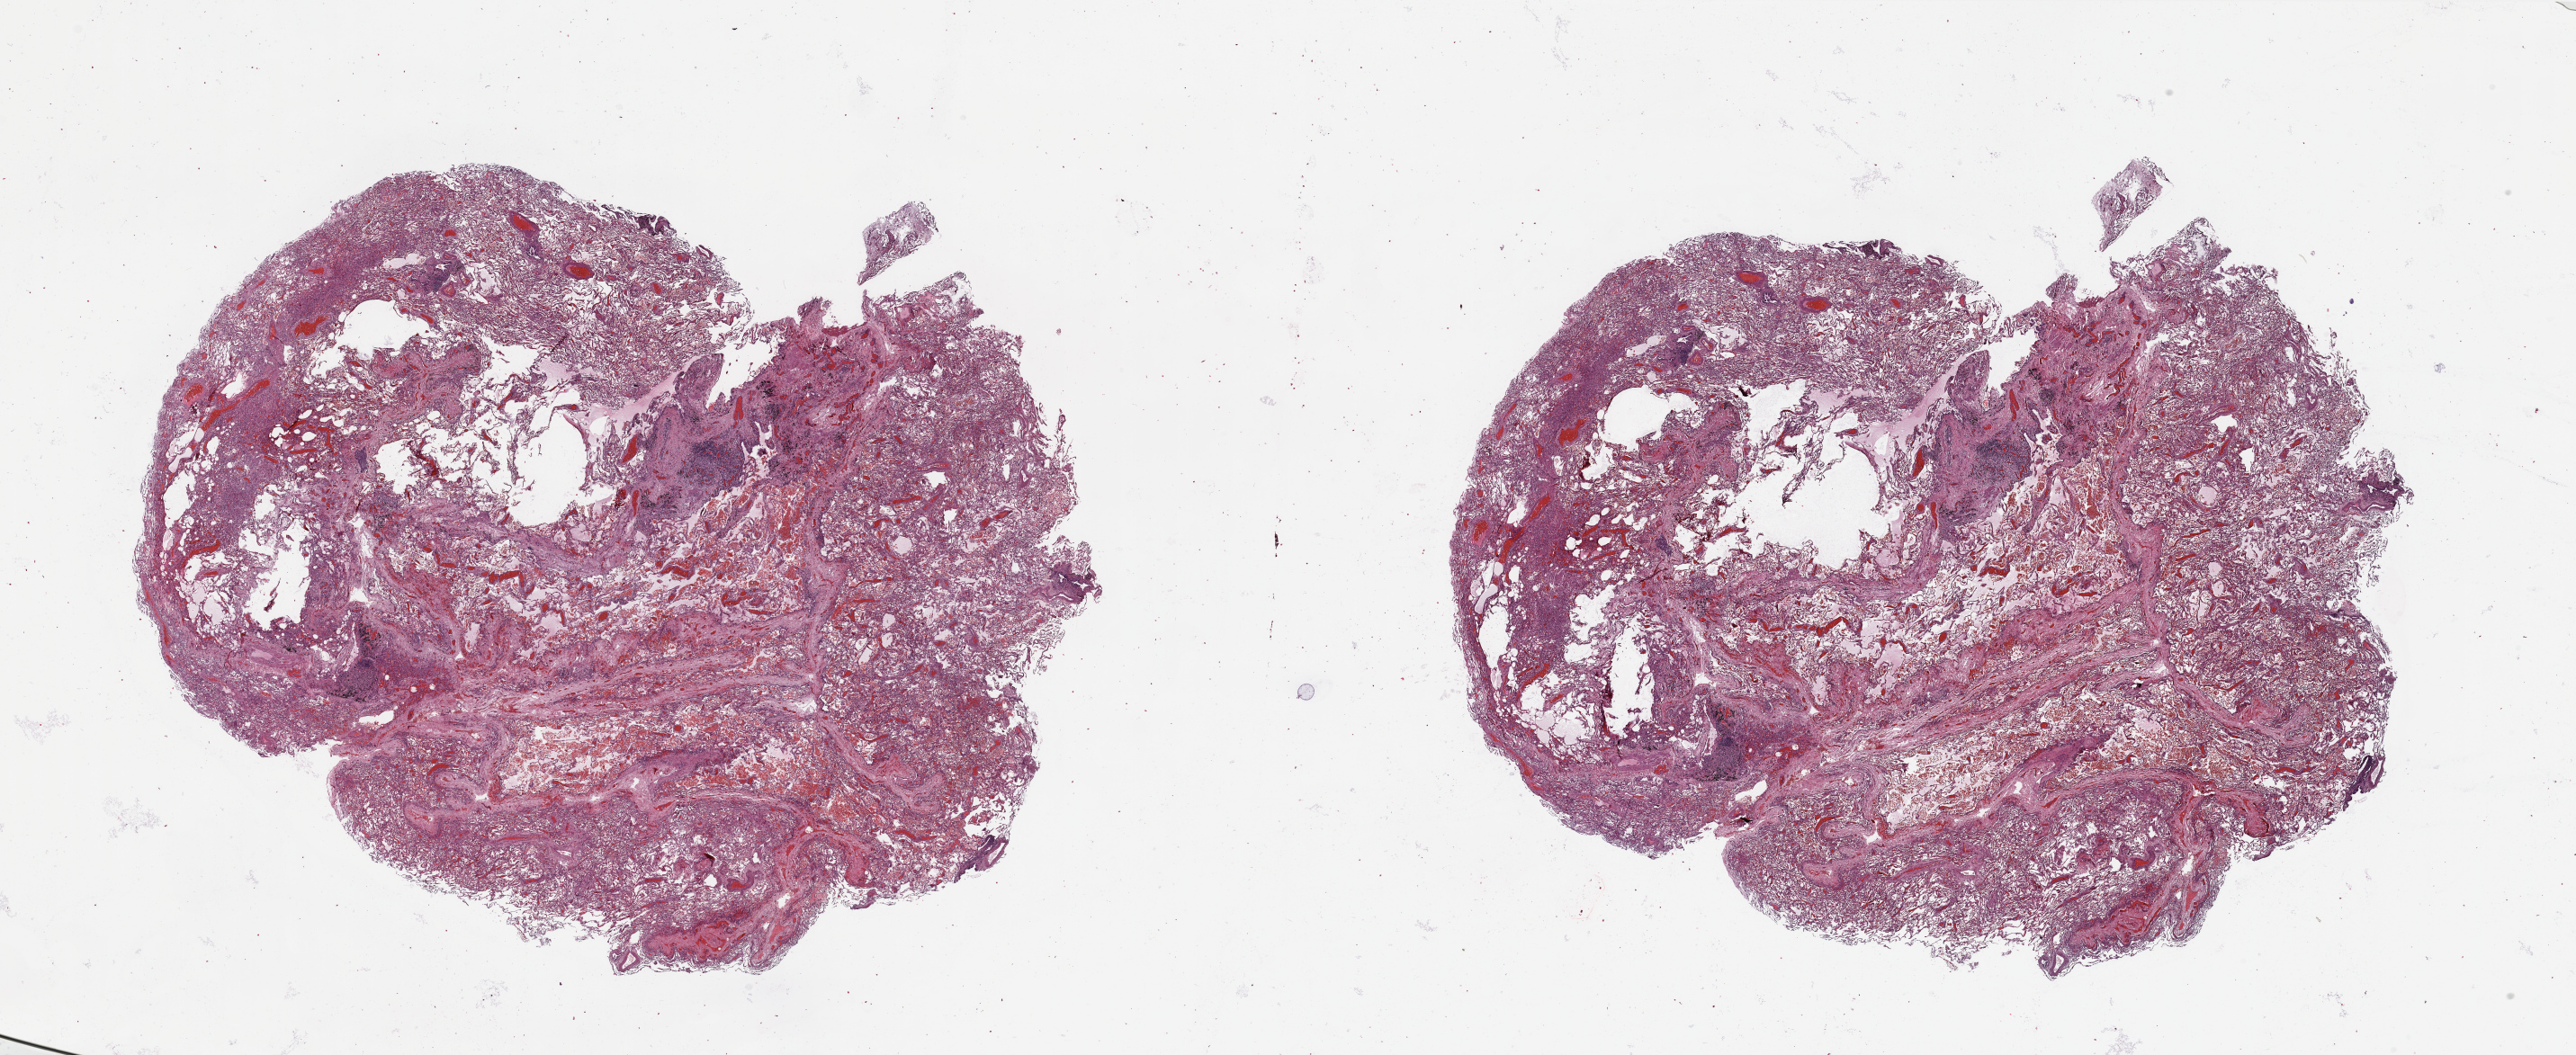
Digitized H&E-stained tissue section (whole slide) — shown as a low-resolution overview of the whole scanned area (about 45.3 x 18.6 mm, acquisition: 20x scan); lung, normal (non-tumour) tissue. Male, 72 y/o.
This section: normal (non-tumour) tissue from the same patient. Patient diagnosis: Adenocarcinoma, NOS.